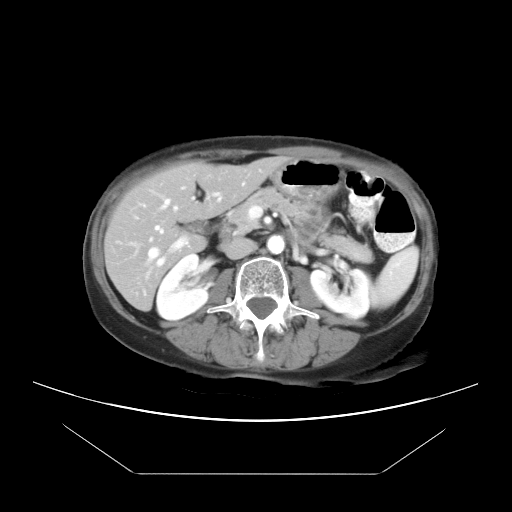
Contrast-enhanced abdominal CT, one axial slice. Position 9 of 21 along the scan axis. 120 kVp. Intravenous contrast given. Soft-tissue window (W 400 / L 40 HU). 7.5 mm slice thickness. 512 × 512 image matrix. Female patient, age 72 years. From the clinical record (not read from this slice): diagnosis: colorectal cancer liver metastases, imaged before liver resection; multiple liver metastases: yes; largest metastasis: 4 cm; disease in both lobes: yes.
Outlined on this slice (manually delineated by an expert):
- hepatic veins: bounding box <132,197,178,279> (left, top, right, bottom; pixels)
- liver: <105,158,281,309>
- planned liver remnant (the part of the liver to remain after resection): <105,158,281,290>
- portal vein (with intrahepatic branches): <139,192,222,266>